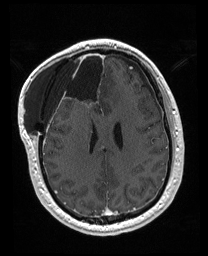
Brain MRI from a brain-tumour surgery series, one axial slice; T1-weighted post-contrast; 1 mm slice thickness; 208 × 256 image matrix, field of view 208 × 256 mm. From the clinical record (not read from this slice): histopathology: Astrocytoma; WHO grade: 4; IDH mutation: yes; tumour location: Right Orbitofrontal Anterior Temporal Insular.
Structures marked on this image (expert manual segmentation):
- previous resection cavity: bounding box [x1, y1, x2, y2] px = [56, 52, 106, 111]